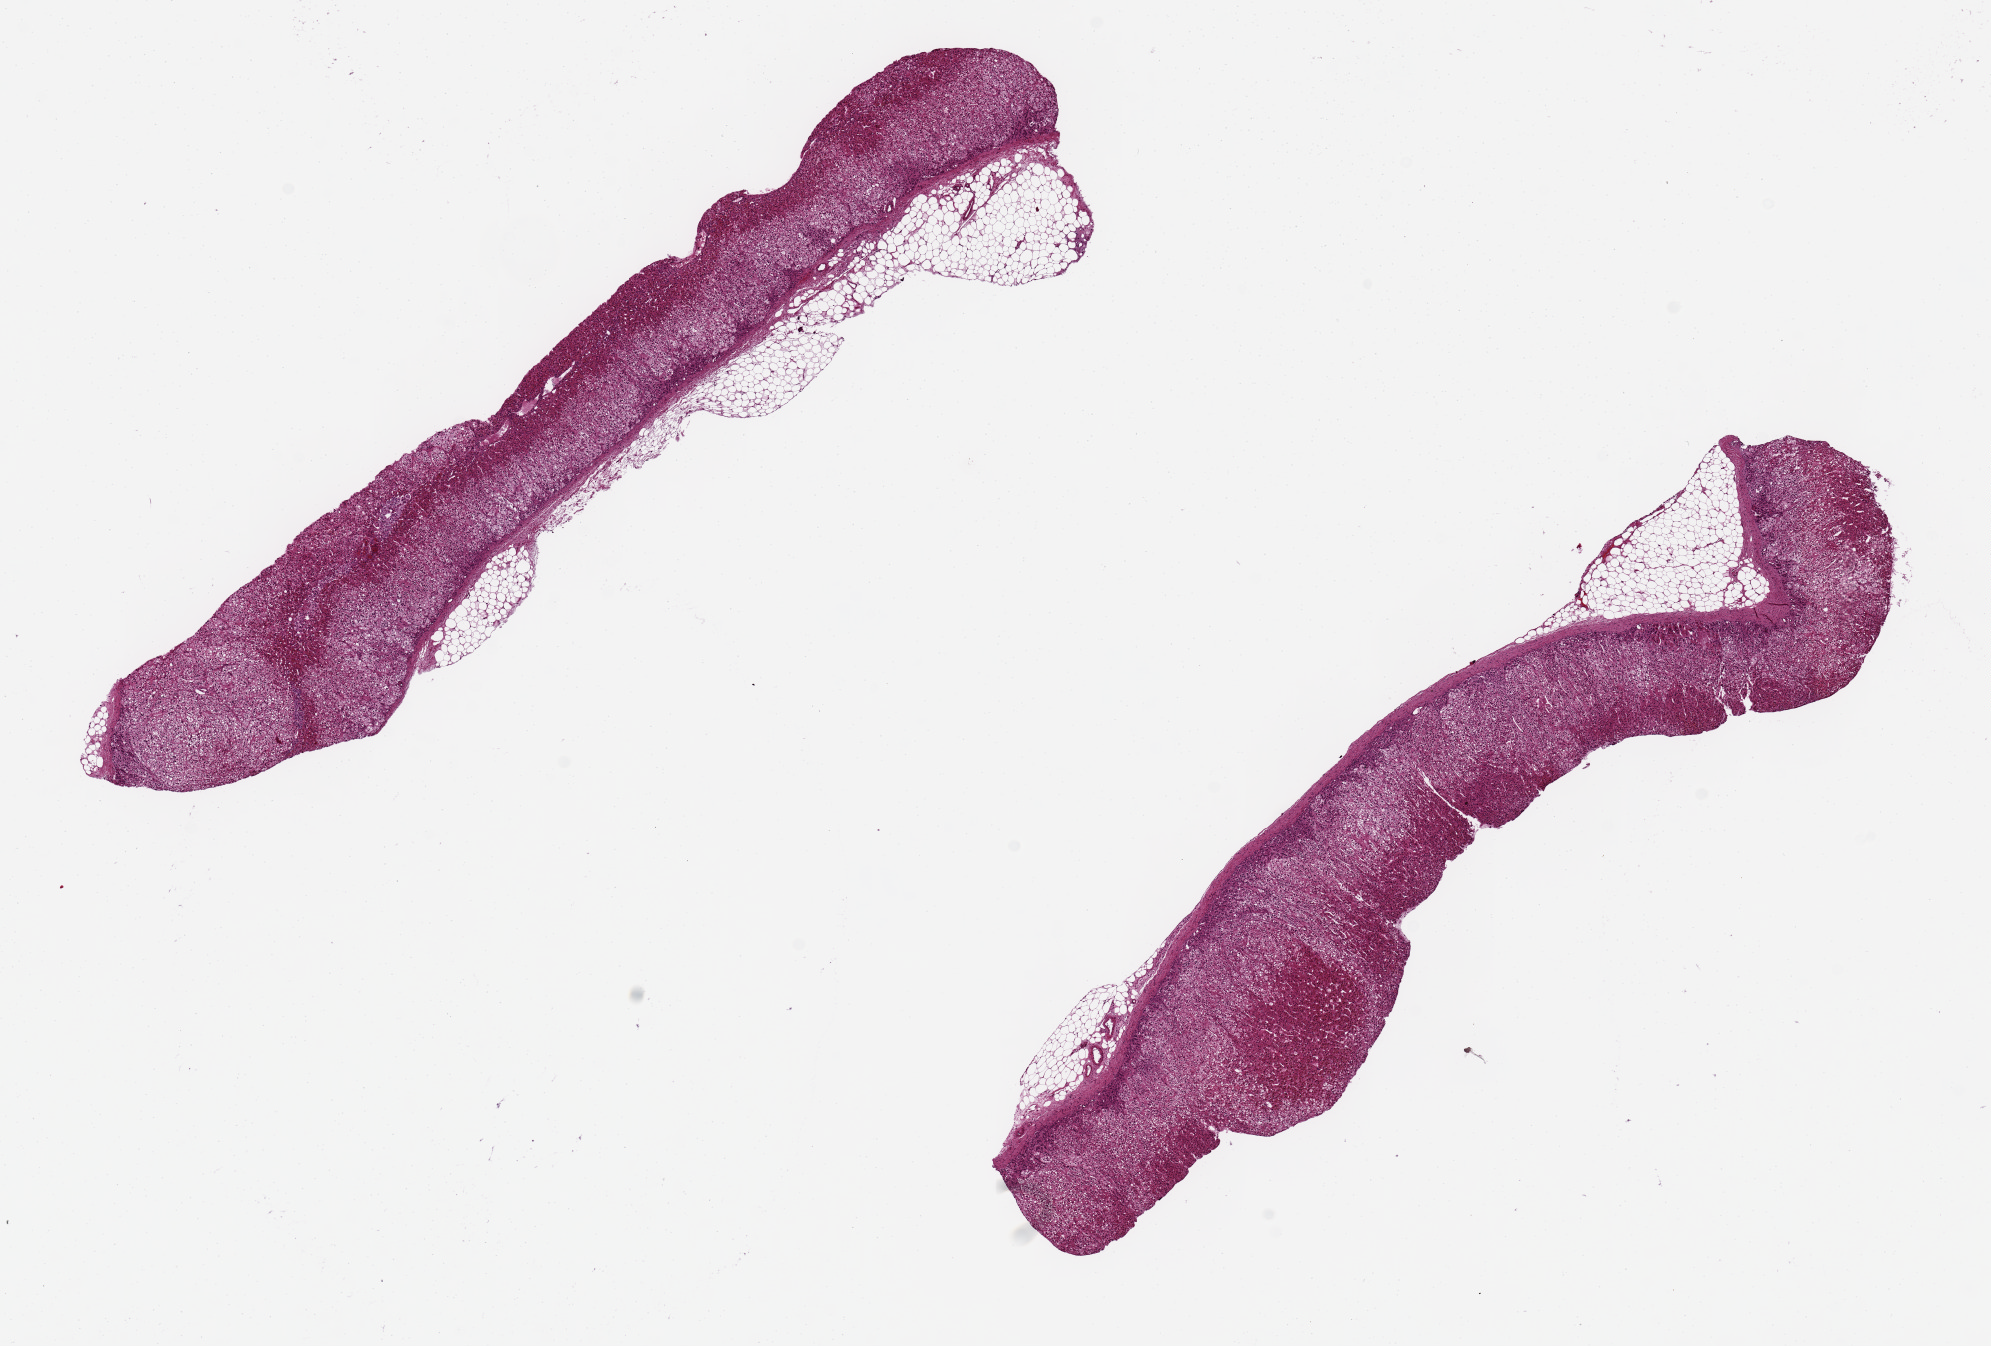
Digitized hematoxylin and eosin (H&E)-stained section, whole scanned area (about 15.8 x 10.6 mm) shown as a low-resolution overview; PAXgene-fixed paraffin-embedded (PFPE) section; sampled site (target tissue): adrenal gland; tissue donor sample. Male donor.
Review note (as recorded): 2 pieces ~9x1 mm; good cortical morphology.